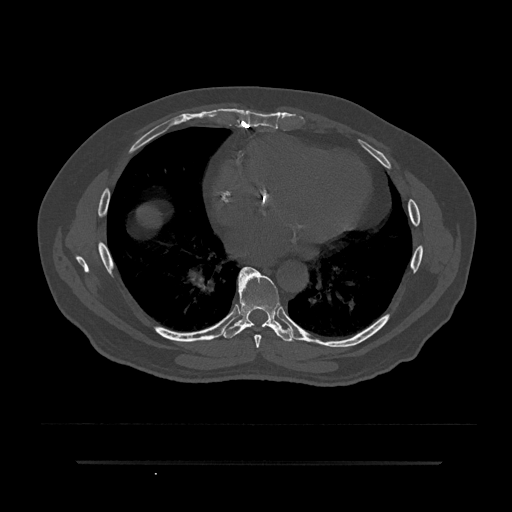
CT including the spine, one axial slice; position 447 of 797 along the scan axis; reconstruction kernel Br40s/3; bone window (W 1800 / L 400 HU); 512 × 512 image matrix, field of view 464 × 464 mm. Male patient, age 59 years. From the clinical record (not read from this slice): primary cancer: bile ducts.
Outlined on this slice (semi-automatically segmented with operator editing):
- T7 vertebra: box from (x=238, y=267) to (x=261, y=348) px
- T8 vertebra: (x=222, y=270)–(x=295, y=342)